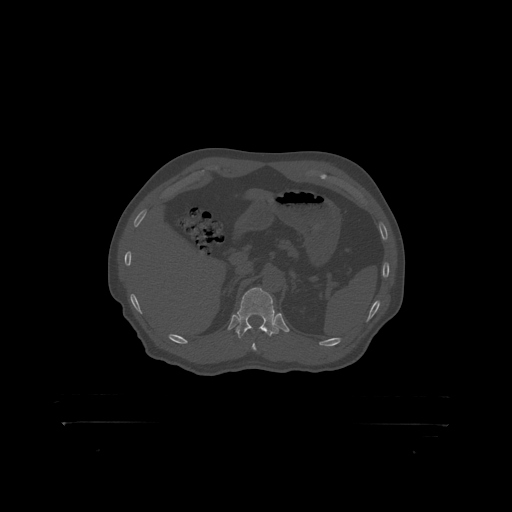
CT including the spine, one axial slice. Slice 358 of 399 in the series (ordered by position). Reconstruction kernel STANDARD. Bone window (W 1800 / L 400 HU). 1.25 mm slice thickness. 512 × 512 image matrix, field of view 650 × 650 mm. Male patient, age 46 years. Case-level facts recorded for this patient, not image findings: primary cancer: skin.
Structures marked on this image (semi-automatic segmentation, software-assisted and operator-edited):
- T12 vertebra: bounding box (x1, y1, x2, y2) in pixels: (238, 288, 281, 319)